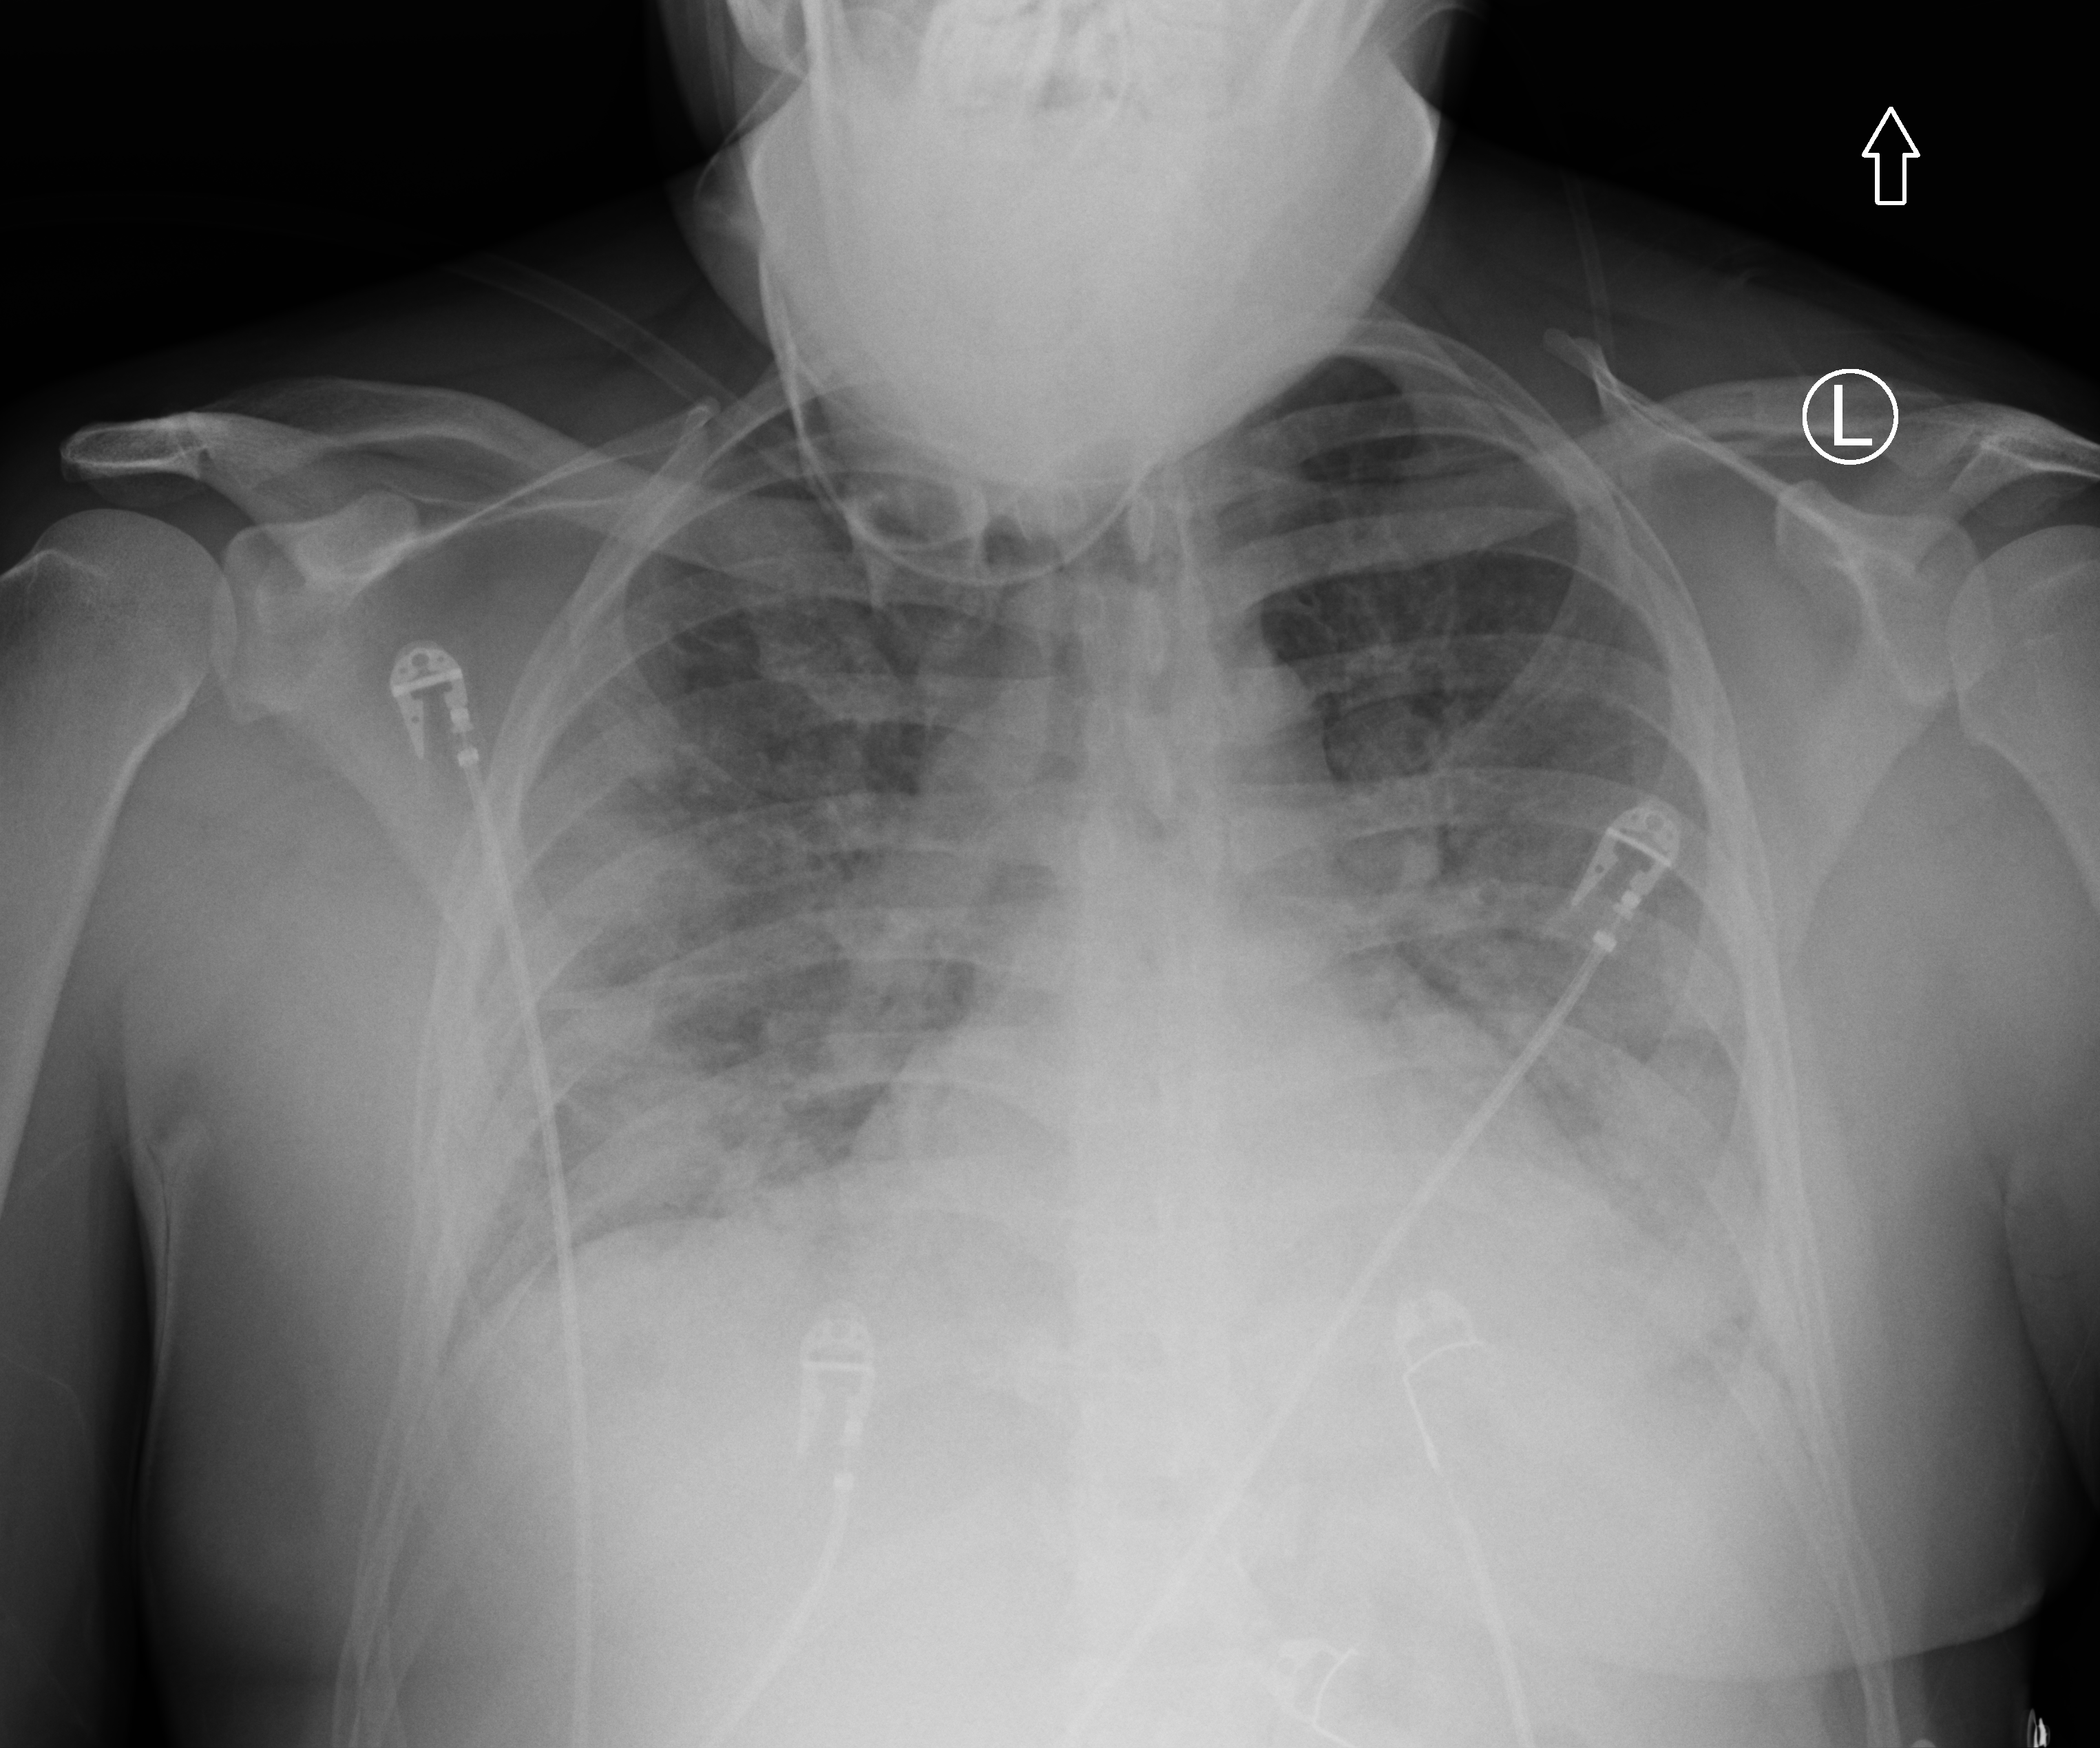
Chest X-ray (portable); anteroposterior (AP) projection. Patient hospitalised with COVID-19; male, aged 18–59 years.
Hospital-stay facts (about this admission, not read from this image; timing relative to this image not recorded): length of hospital stay: 30 days; admitted to intensive care during this hospital stay: yes; mechanically ventilated during this hospital stay: yes.